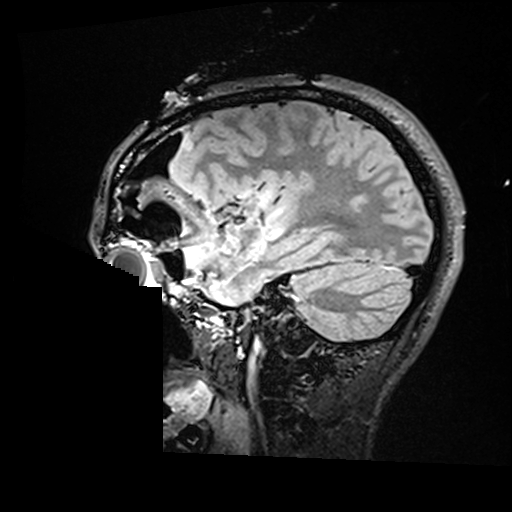
Brain MRI from a brain-tumour surgery series, one sagittal slice. Position 119 of 176 along the scan axis. T2 FLAIR. 1 mm slice thickness. 512 × 512 image matrix. From the clinical record (not read from this slice): histopathology: Astrocytoma; WHO grade: 2; IDH mutation: yes.
Outlined on this slice (manually delineated by an expert):
- residual tumour: bounding box [x1, y1, x2, y2] px = [259, 189, 282, 221]